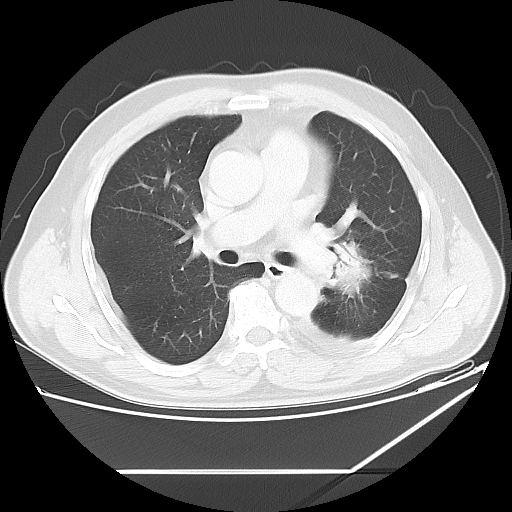
Chest CT, one axial slice. Slice 34 of 60 in the series (ordered by position). Reconstruction kernel LUNG. 120 kVp. Lung window (W 1500 / L -600 HU). 512 × 512 image matrix, field of view 395 × 395 mm. Male patient, age 62 years. Case-level facts recorded for this patient, not image findings: clinical TNM (as recorded): T3 N0 M1.
Structures marked on this image (bounding box drawn by a radiologist):
- lung tumour (recorded histology: adenocarcinoma): box from (x=326, y=236) to (x=373, y=300) px
- lung tumour (recorded histology: adenocarcinoma): (x=332, y=233)–(x=375, y=298)